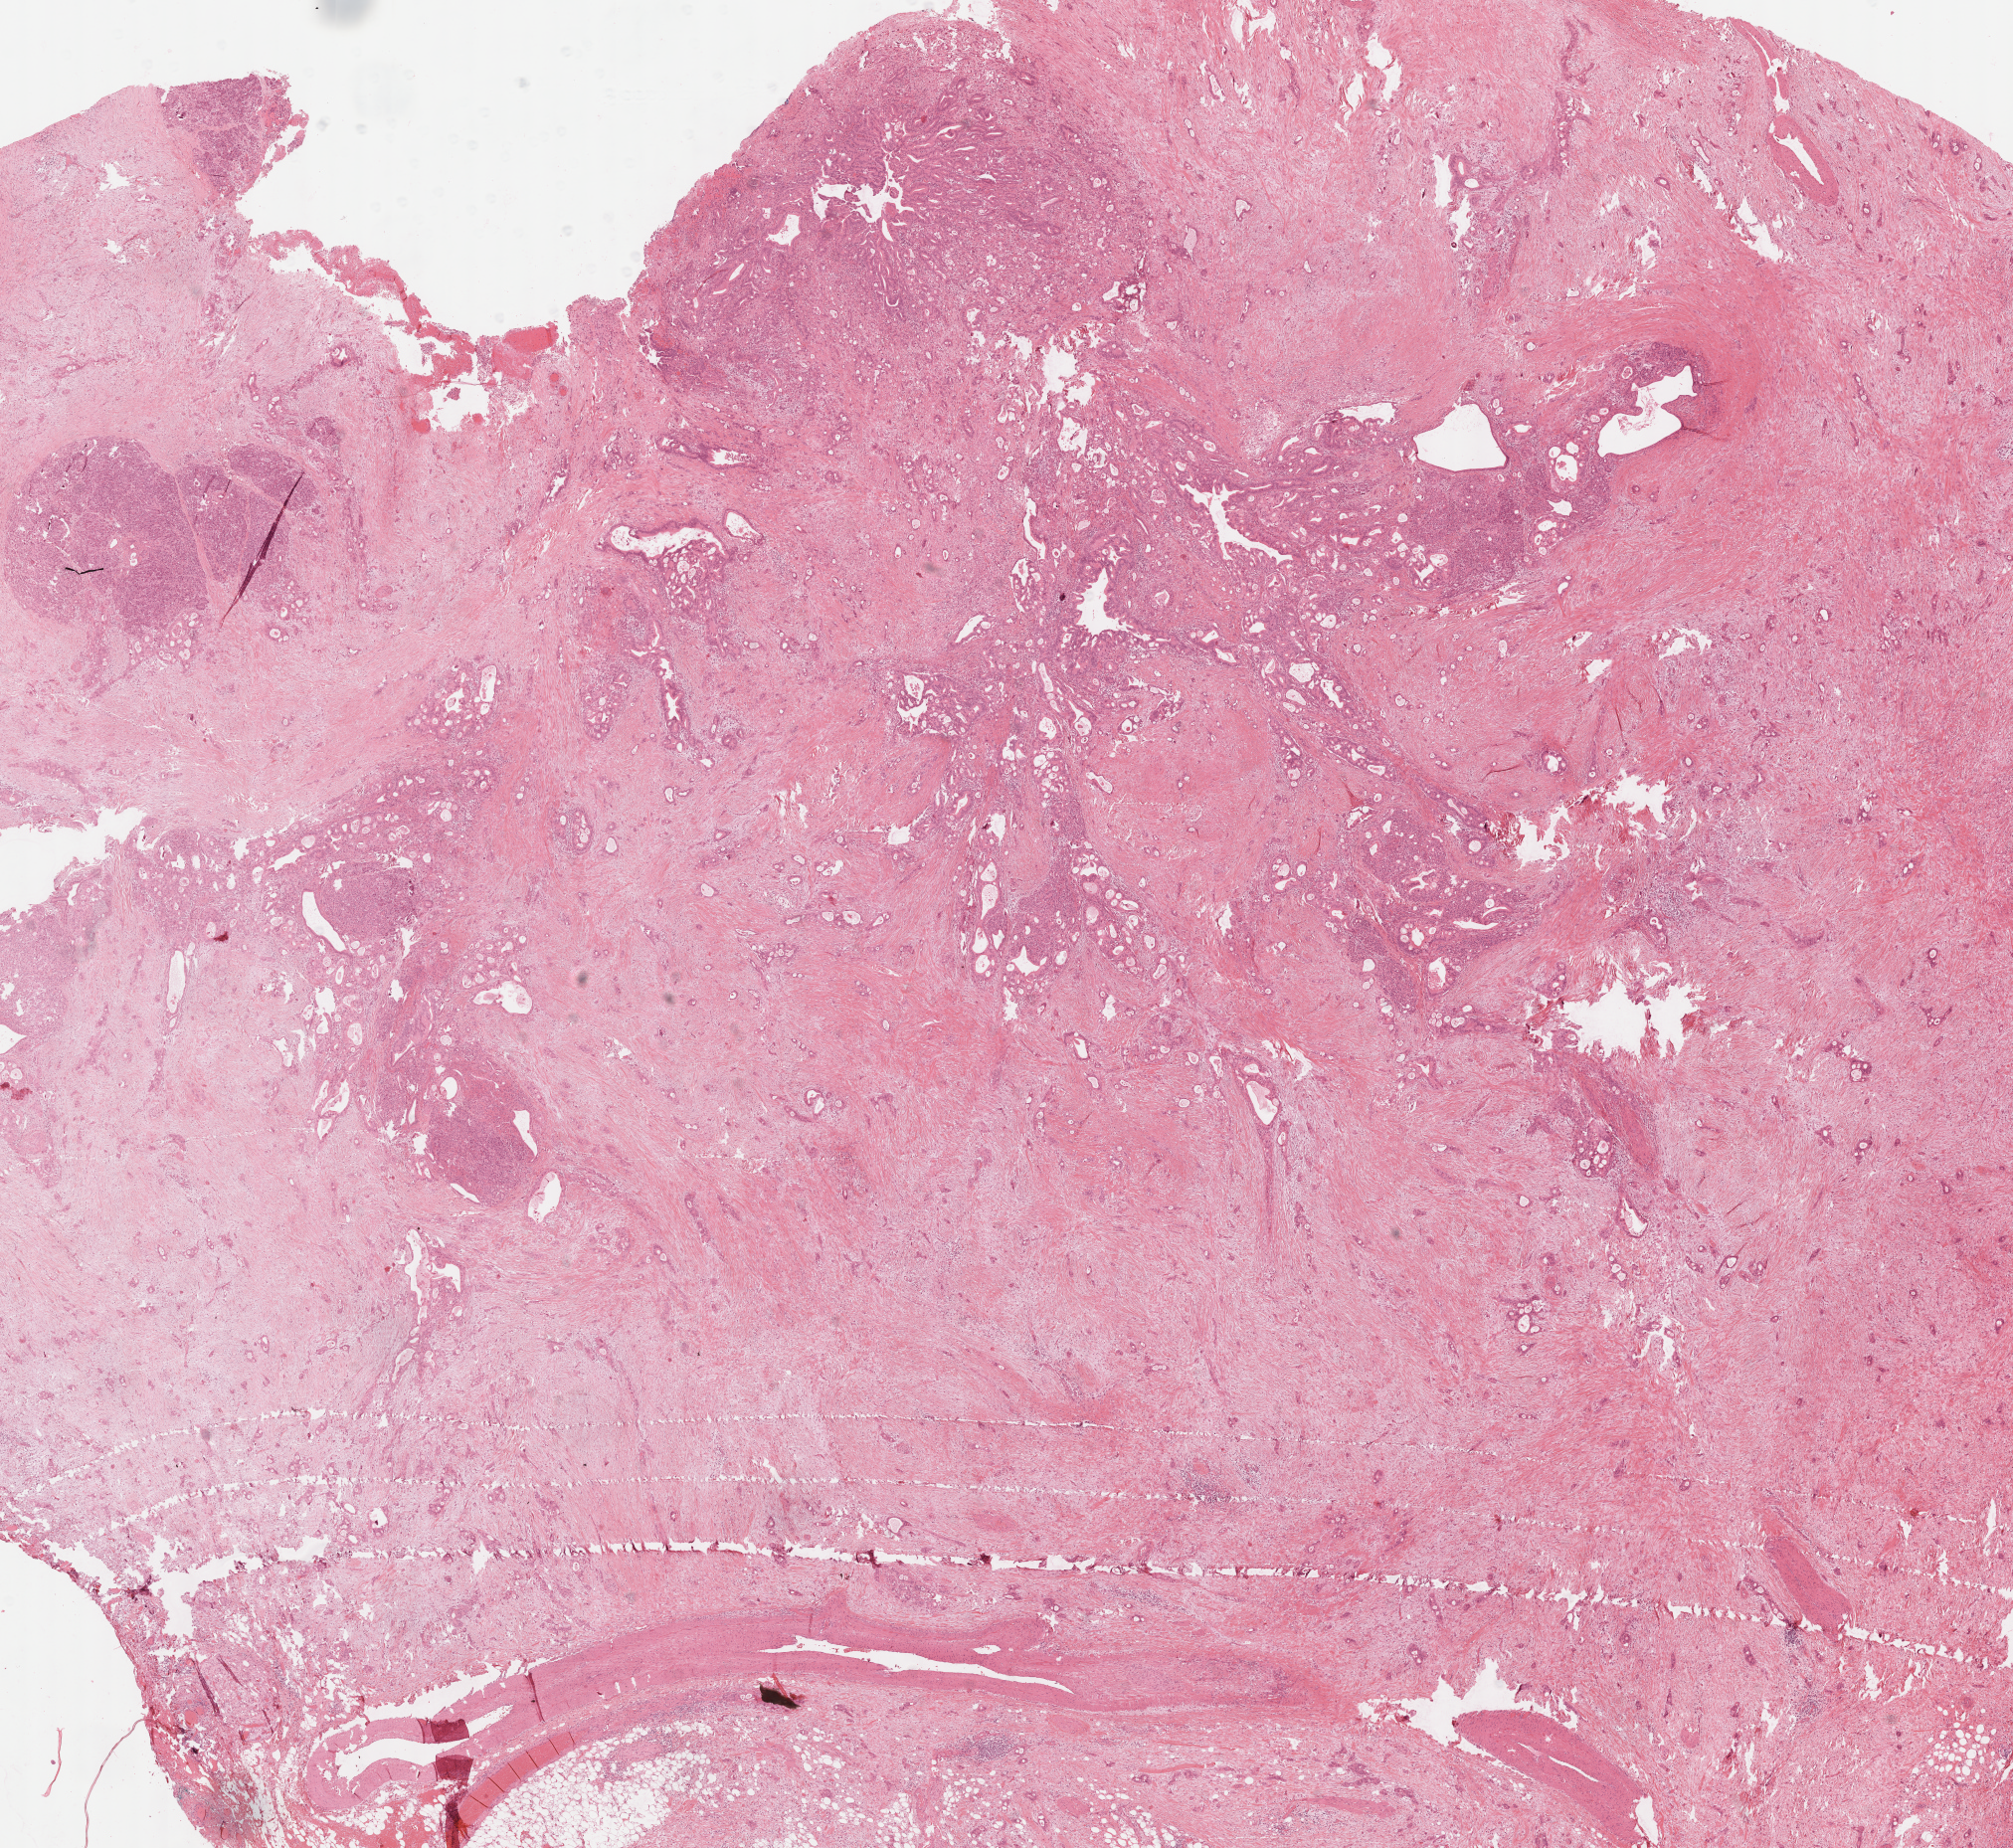
Hematoxylin and eosin (H&E) stained whole-slide image — shown as a low-resolution overview of the whole scanned area (about 16.1 x 14.8 mm). Formalin-fixed paraffin-embedded (FFPE) diagnostic section. Sample: primary tumour, pancreas. Patient: male, age at initial diagnosis 56 years. Histologic grade: G2 (moderately differentiated).
Pathologic diagnosis: Infiltrating duct carcinoma, NOS. AJCC pathologic stage: IIB (7th edition).